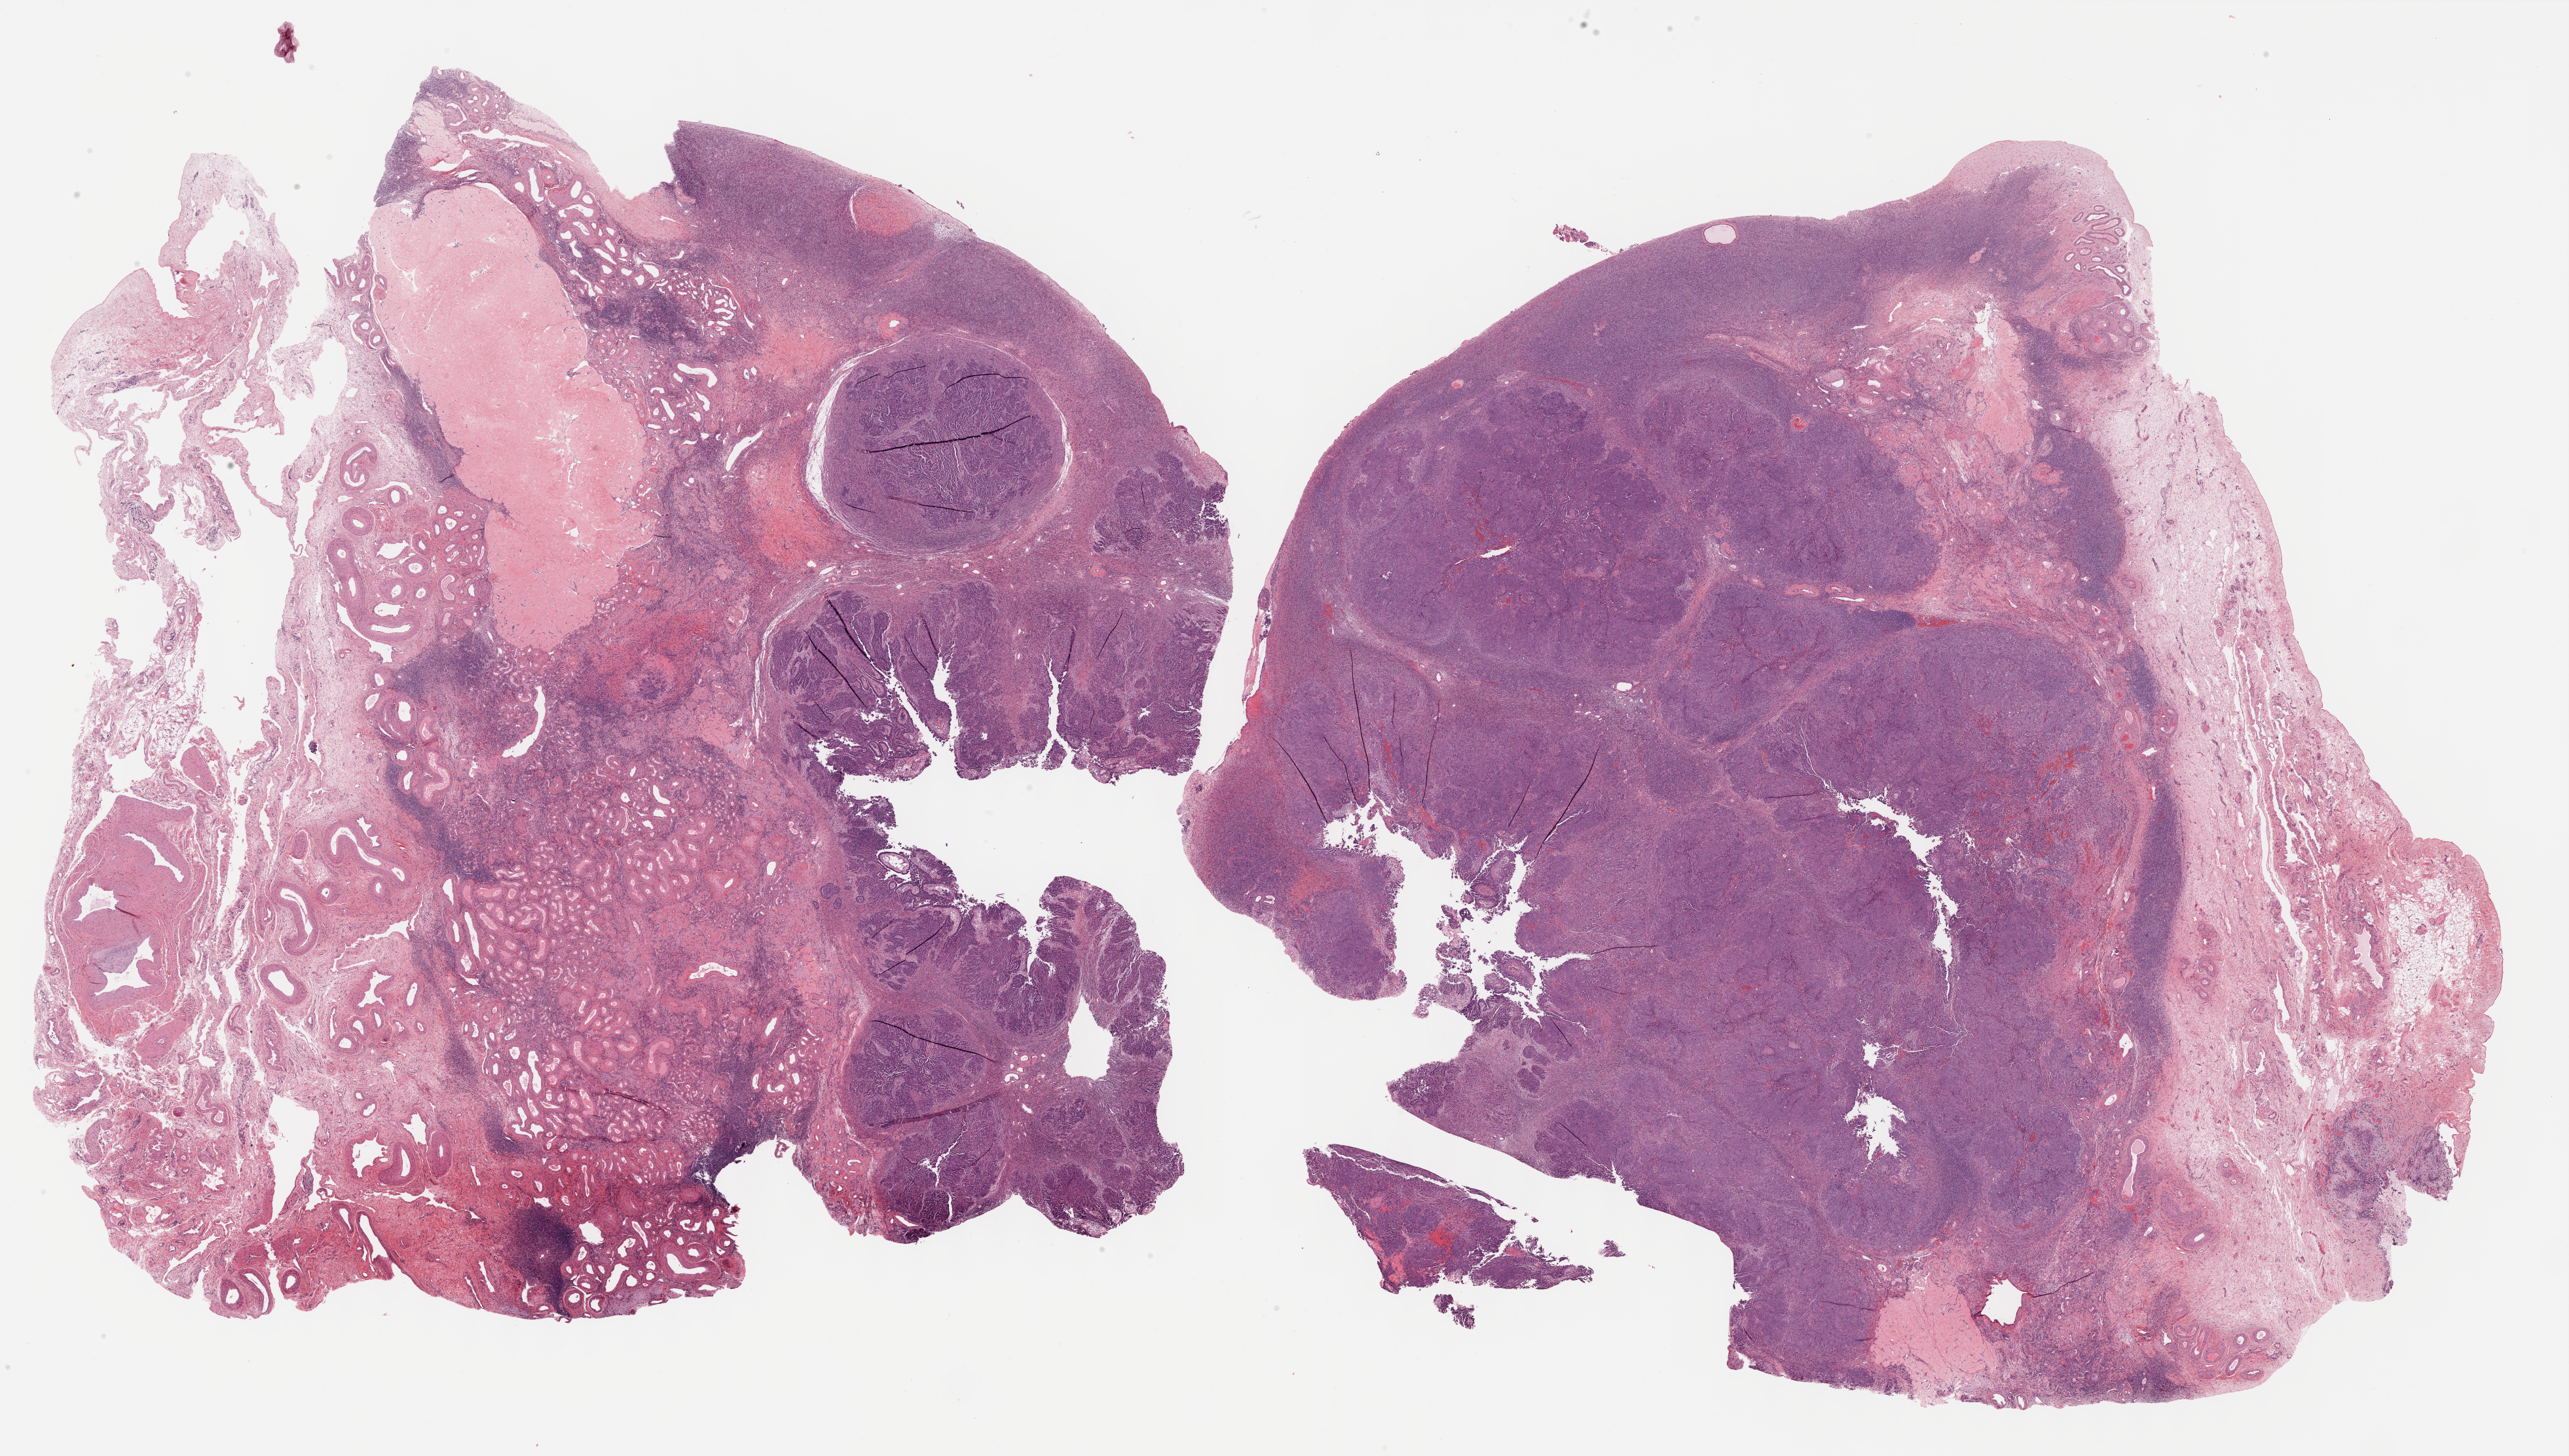
Whole-slide histology image, H&E-stained, shown as a low-resolution overview of the whole scanned area (about 31.7 x 18.0 mm, slide scanned at 40x), FFPE section, ovary, primary tumour sample. Female, age 71 years at initial diagnosis. Histologic grade: G3 (poorly differentiated).
- FIGO stage: IV
- diagnosis: Serous cystadenocarcinoma, NOS